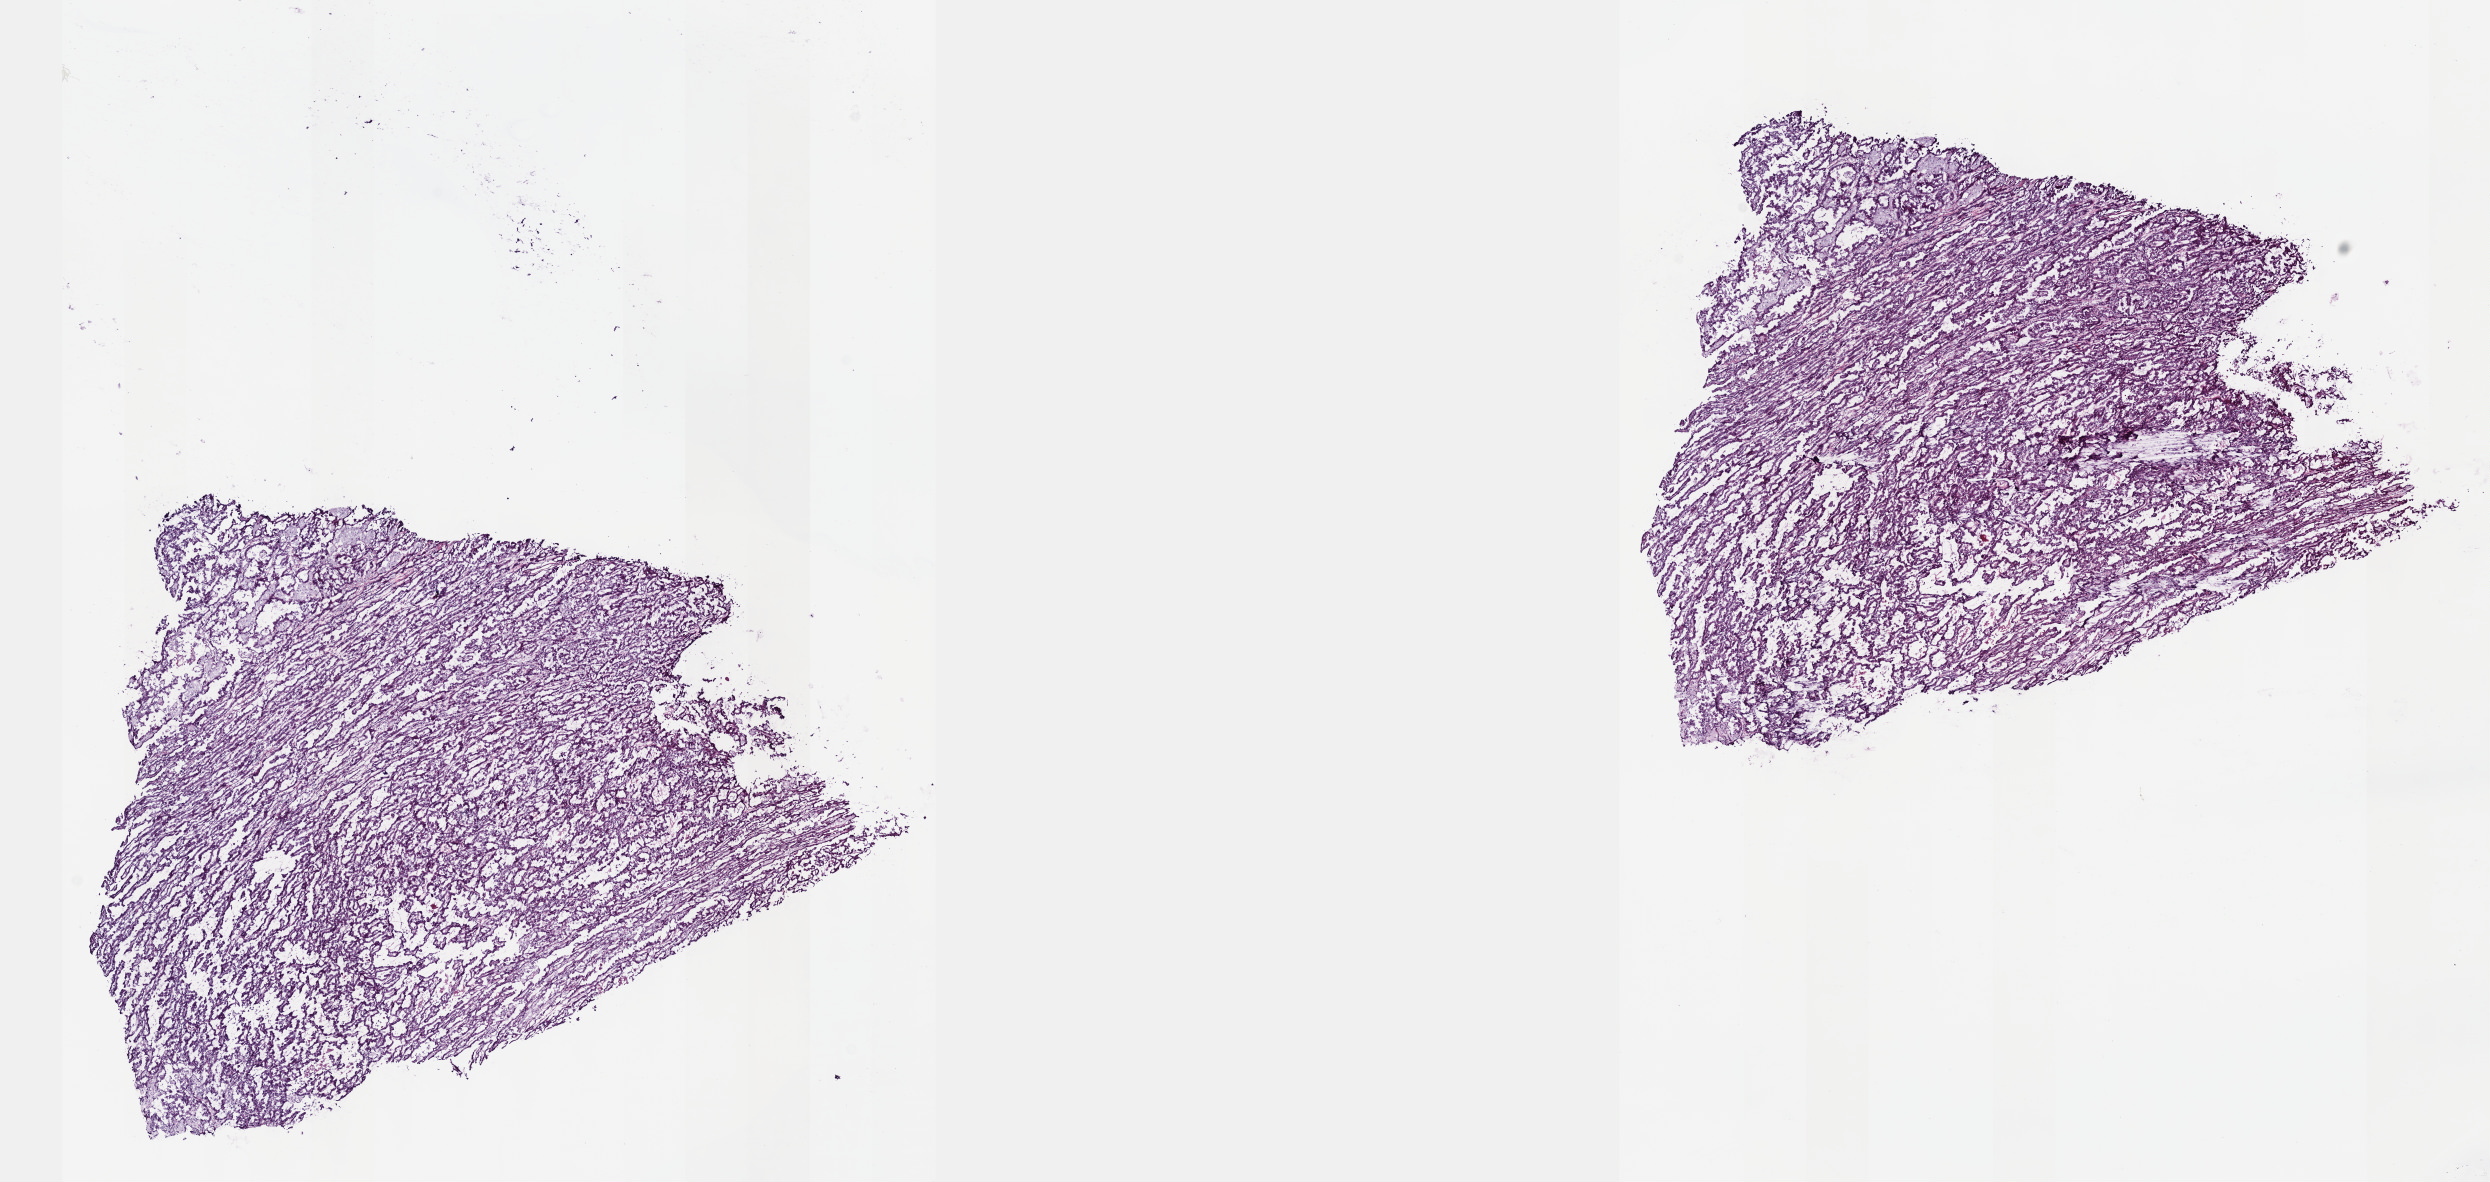
Digitized Hematoxylin and eosin (H&E) stained tissue section (whole slide) — shown as a low-resolution overview of the whole scanned area (about 20.1 x 9.6 mm, acquisition: 40x scan); frozen section from the top of the tissue portion; kidney, additional new primary tumour sample. Female, age 62 years at initial diagnosis. Slide review estimates, as recorded: tumour cells 90%, tumour nuclei 95%, normal cells 0%, stromal cells 10%, necrosis 0%. Inflammatory infiltration, as recorded: lymphocyte infiltration 0%, monocyte infiltration 0%, neutrophil infiltration 0%.
This section: additional new primary tumour. Patient diagnosis: Papillary adenocarcinoma, NOS.